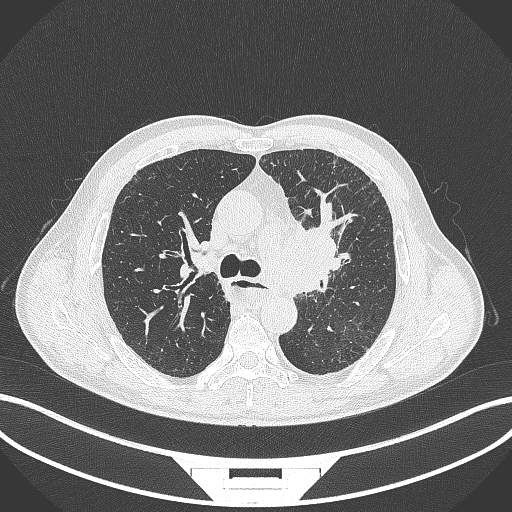
Chest CT, one axial slice. Slice 250 of 411 in the series (ordered by position). Reconstruction kernel B70f. Lung window (W 1500 / L -600 HU). 512 × 512 image matrix, field of view 400 × 400 mm. Male patient, age 57 years. From the clinical record (not read from this slice): clinical TNM (as recorded): T2a N1 M0.
Outlined on this slice (bounding box drawn by a radiologist):
- lung tumour (recorded histology: squamous cell carcinoma): box from (x=277, y=207) to (x=353, y=299) px